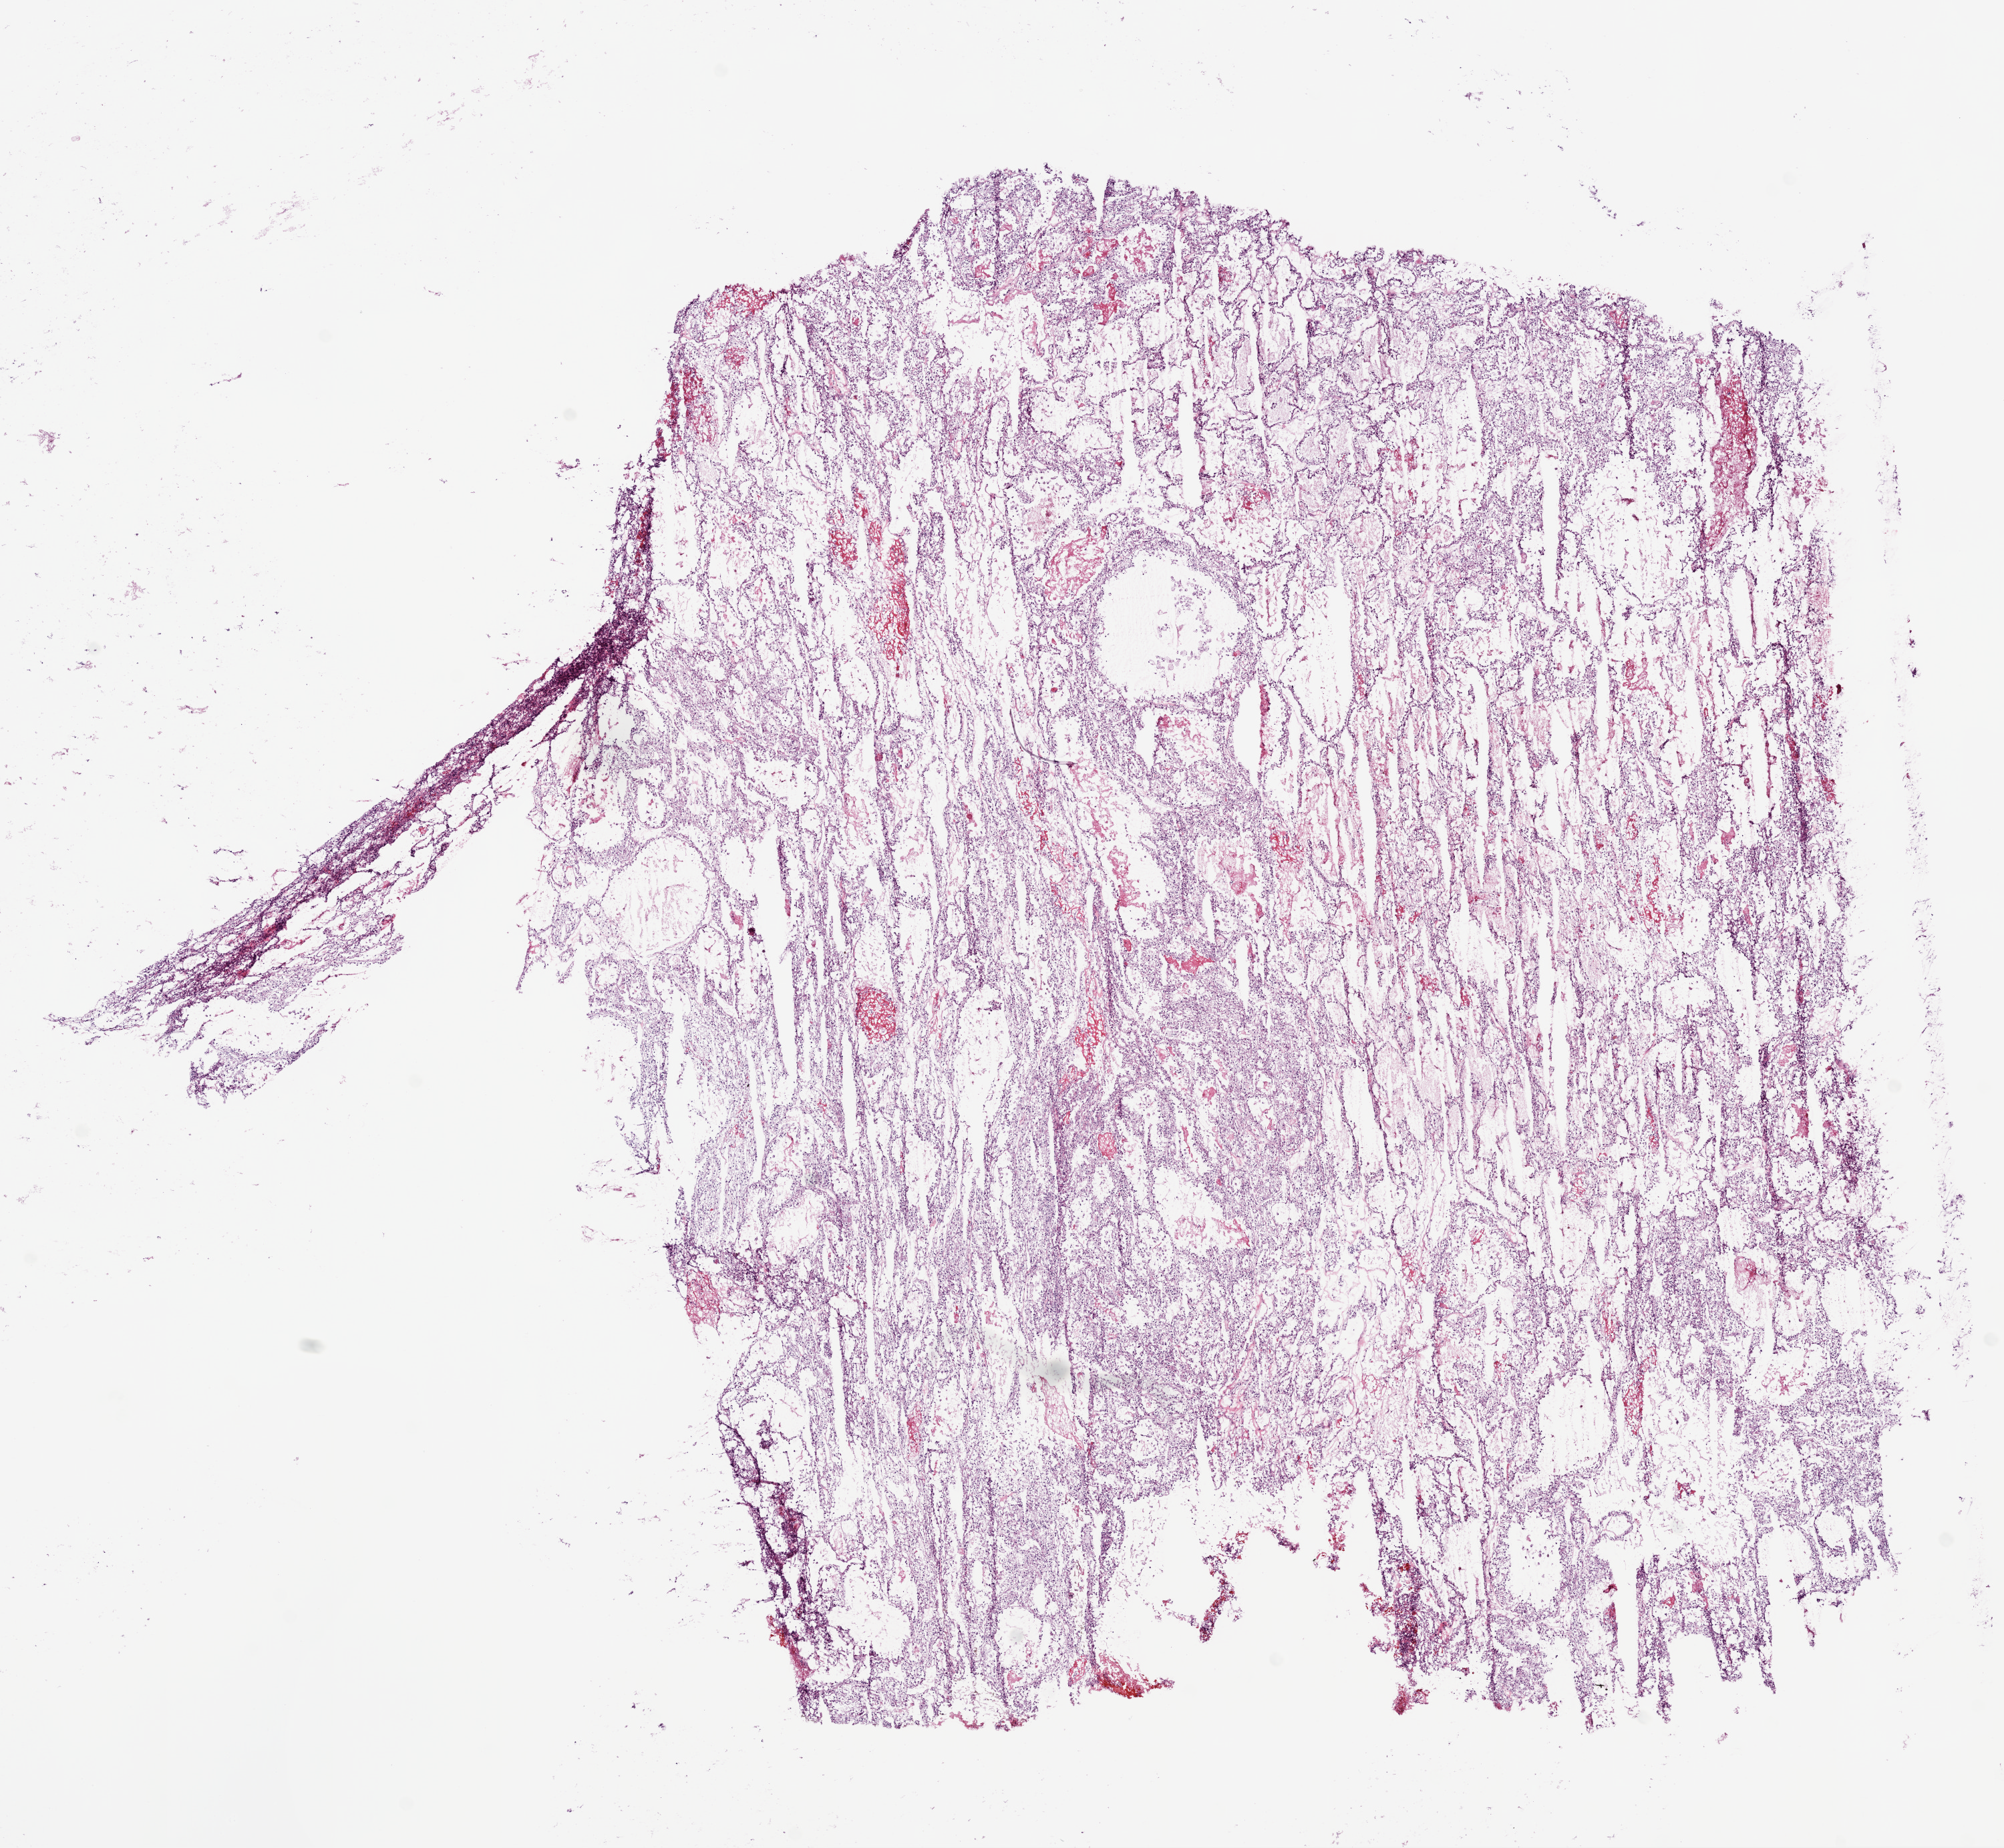
H&E-stained whole-slide image, shown as a low-resolution overview of the whole scanned area (about 12.0 x 11.1 mm). Frozen section from the bottom of the tissue portion. Sample: primary tumour, kidney. Male, age 62 years at initial diagnosis. Histologic grade: G3 (poorly differentiated). Slide review estimates, as recorded: tumour cells 95%, tumour nuclei 85%, normal cells 0%, stromal cells 5%, necrosis 0%.
- histologic diagnosis: Clear cell adenocarcinoma, NOS
- laterality: right
- AJCC pathologic stage: II